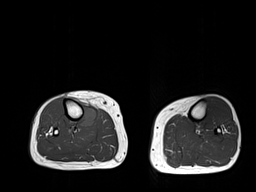
MRI of an extremity soft-tissue mass, one axial slice; position 16 of 32 along the scan axis; 256 × 192 image matrix, field of view 375 × 281 mm. Female patient. Case-level facts recorded for this patient, not image findings: histological type: undifferentiated – high grade; grade: high; site of the primary tumour: right thigh.
Annotated regions visible in this slice (expert manual segmentation):
- gross tumour volume (mass): bounding box <78,102,97,127> (left, top, right, bottom; pixels)